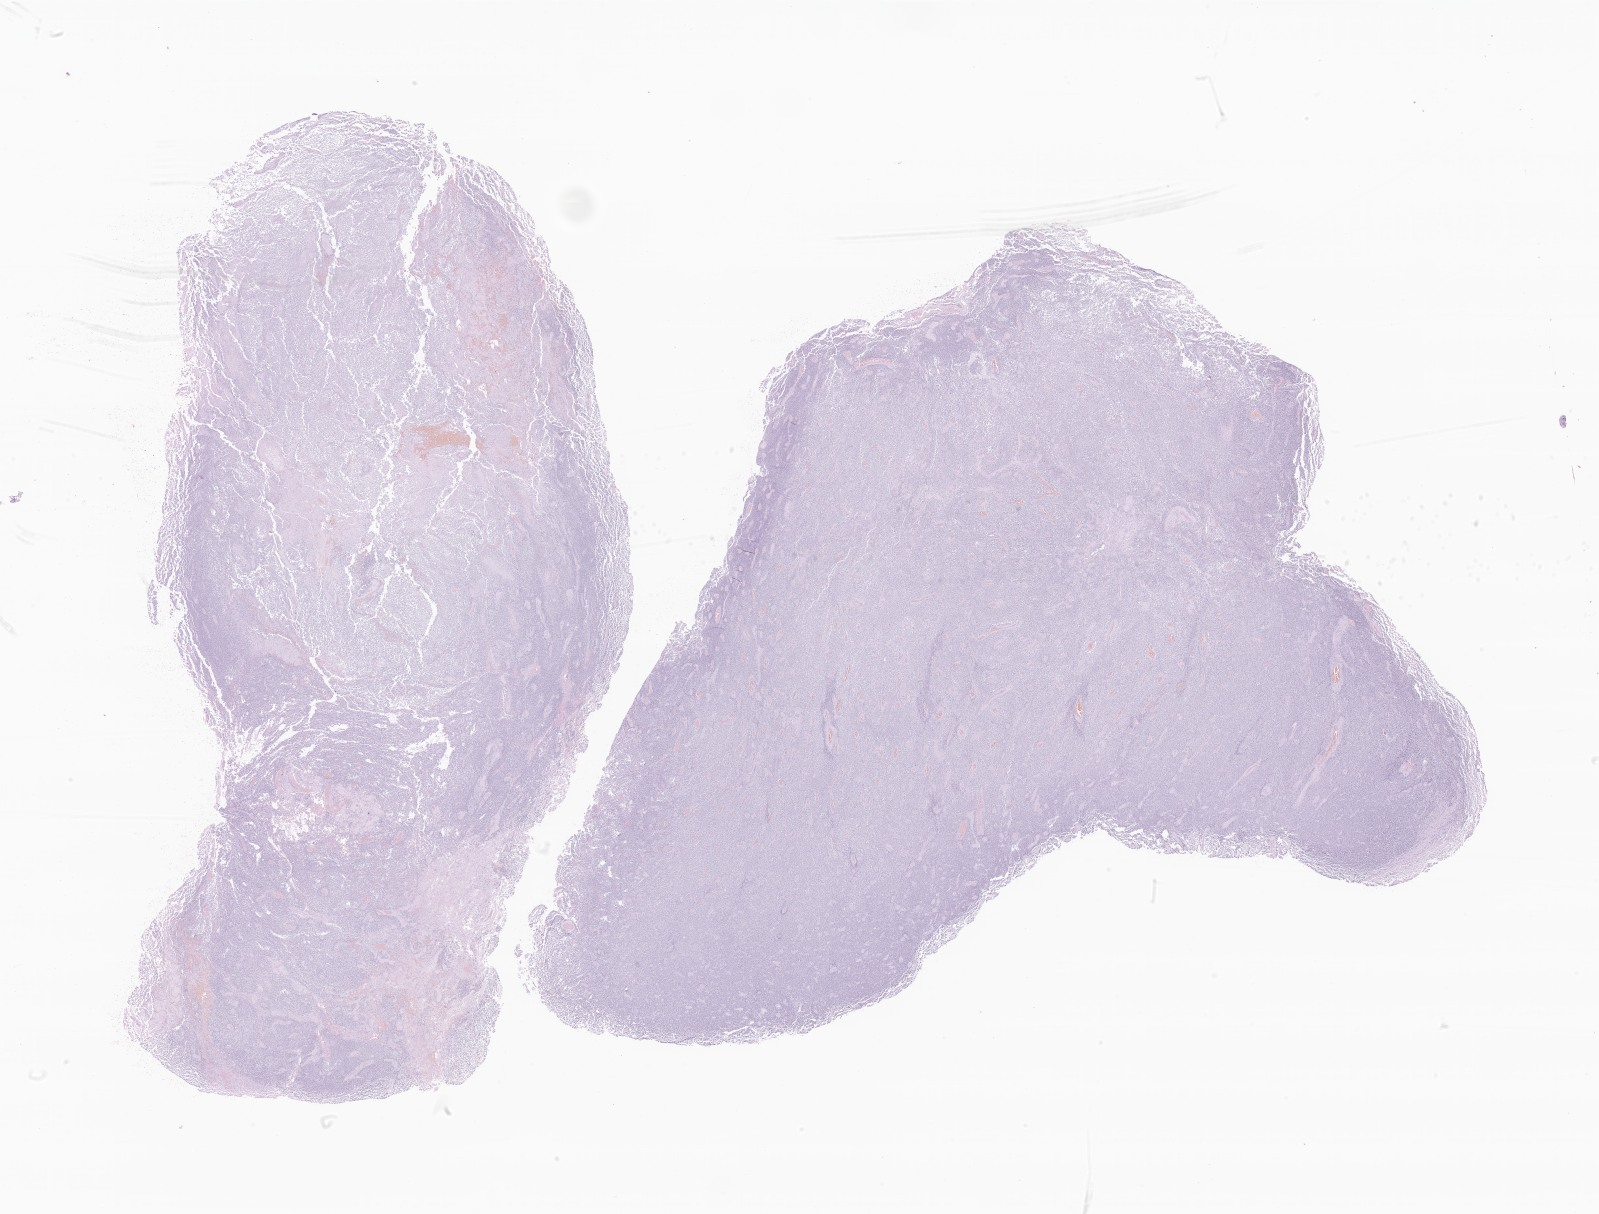
Digitized haematoxylin and eosin-stained section of tumor tissue from the cerebrum — shown as a low-resolution overview of the whole scanned area (about 27.0 x 20.5 mm). Formalin-fixed, paraffin-embedded (FFPE) tissue. Patient: female, age 72 months (6 years).
Recorded diagnosis: Neoplasm, malignant.